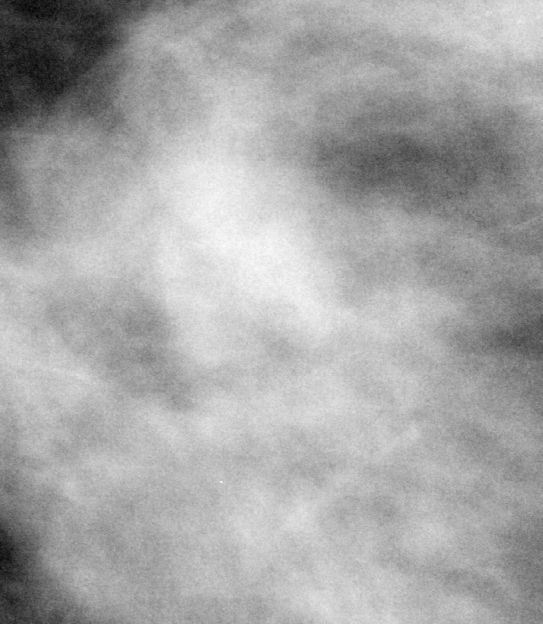
Region of interest cut from a scanned film mammogram (one marked finding); left breast; MLO view; BI-RADS breast density category 3 (scale 1–4).
Mass, shape irregular, margins ill defined; BI-RADS assessment category 4; pathology result (as recorded, not read from the image): malignant.